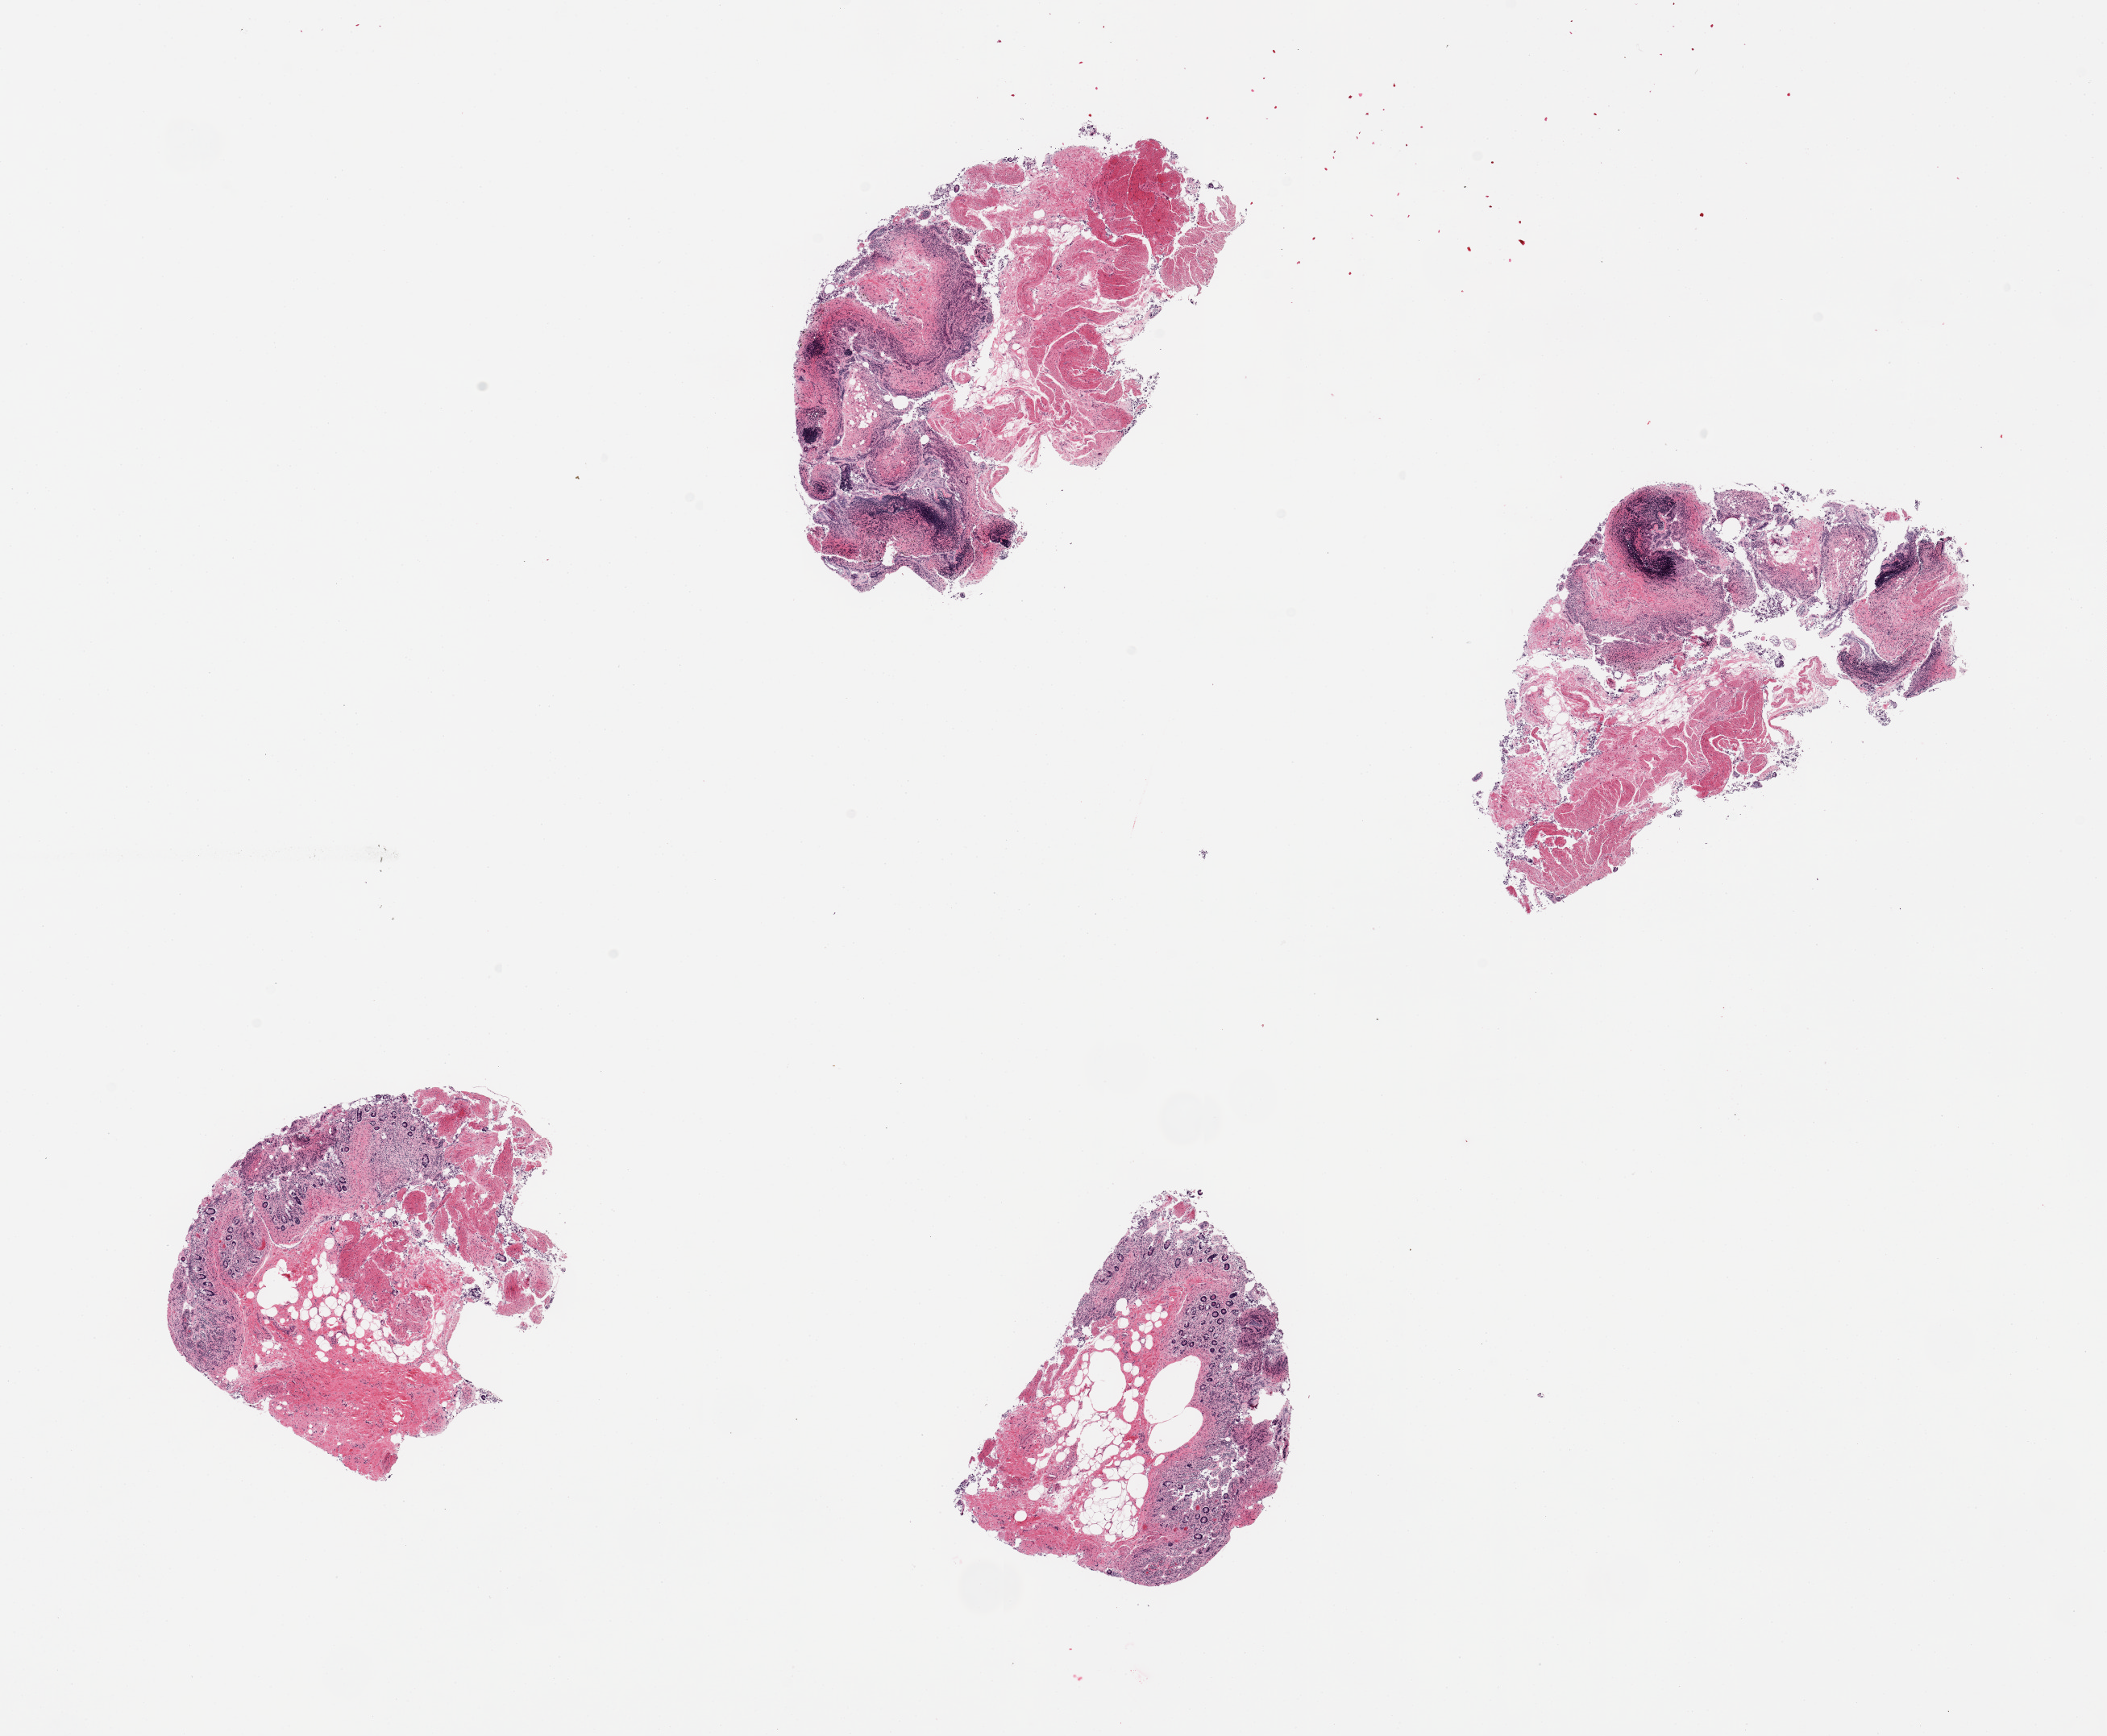
Digitized hematoxylin and eosin (H&E)-stained section, brightfield — whole scanned area (about 20.7 x 17.0 mm) shown as a low-resolution overview. PAXgene-fixed, paraffin-embedded tissue. Section of ileum (target tissue). Donor tissue sample. Donor sex: male.
- reviewer comment on this tissue sample: 4 pieces; predominantly autolyzed mucosa with some residual lymphoid tissue and muscularis (not target)